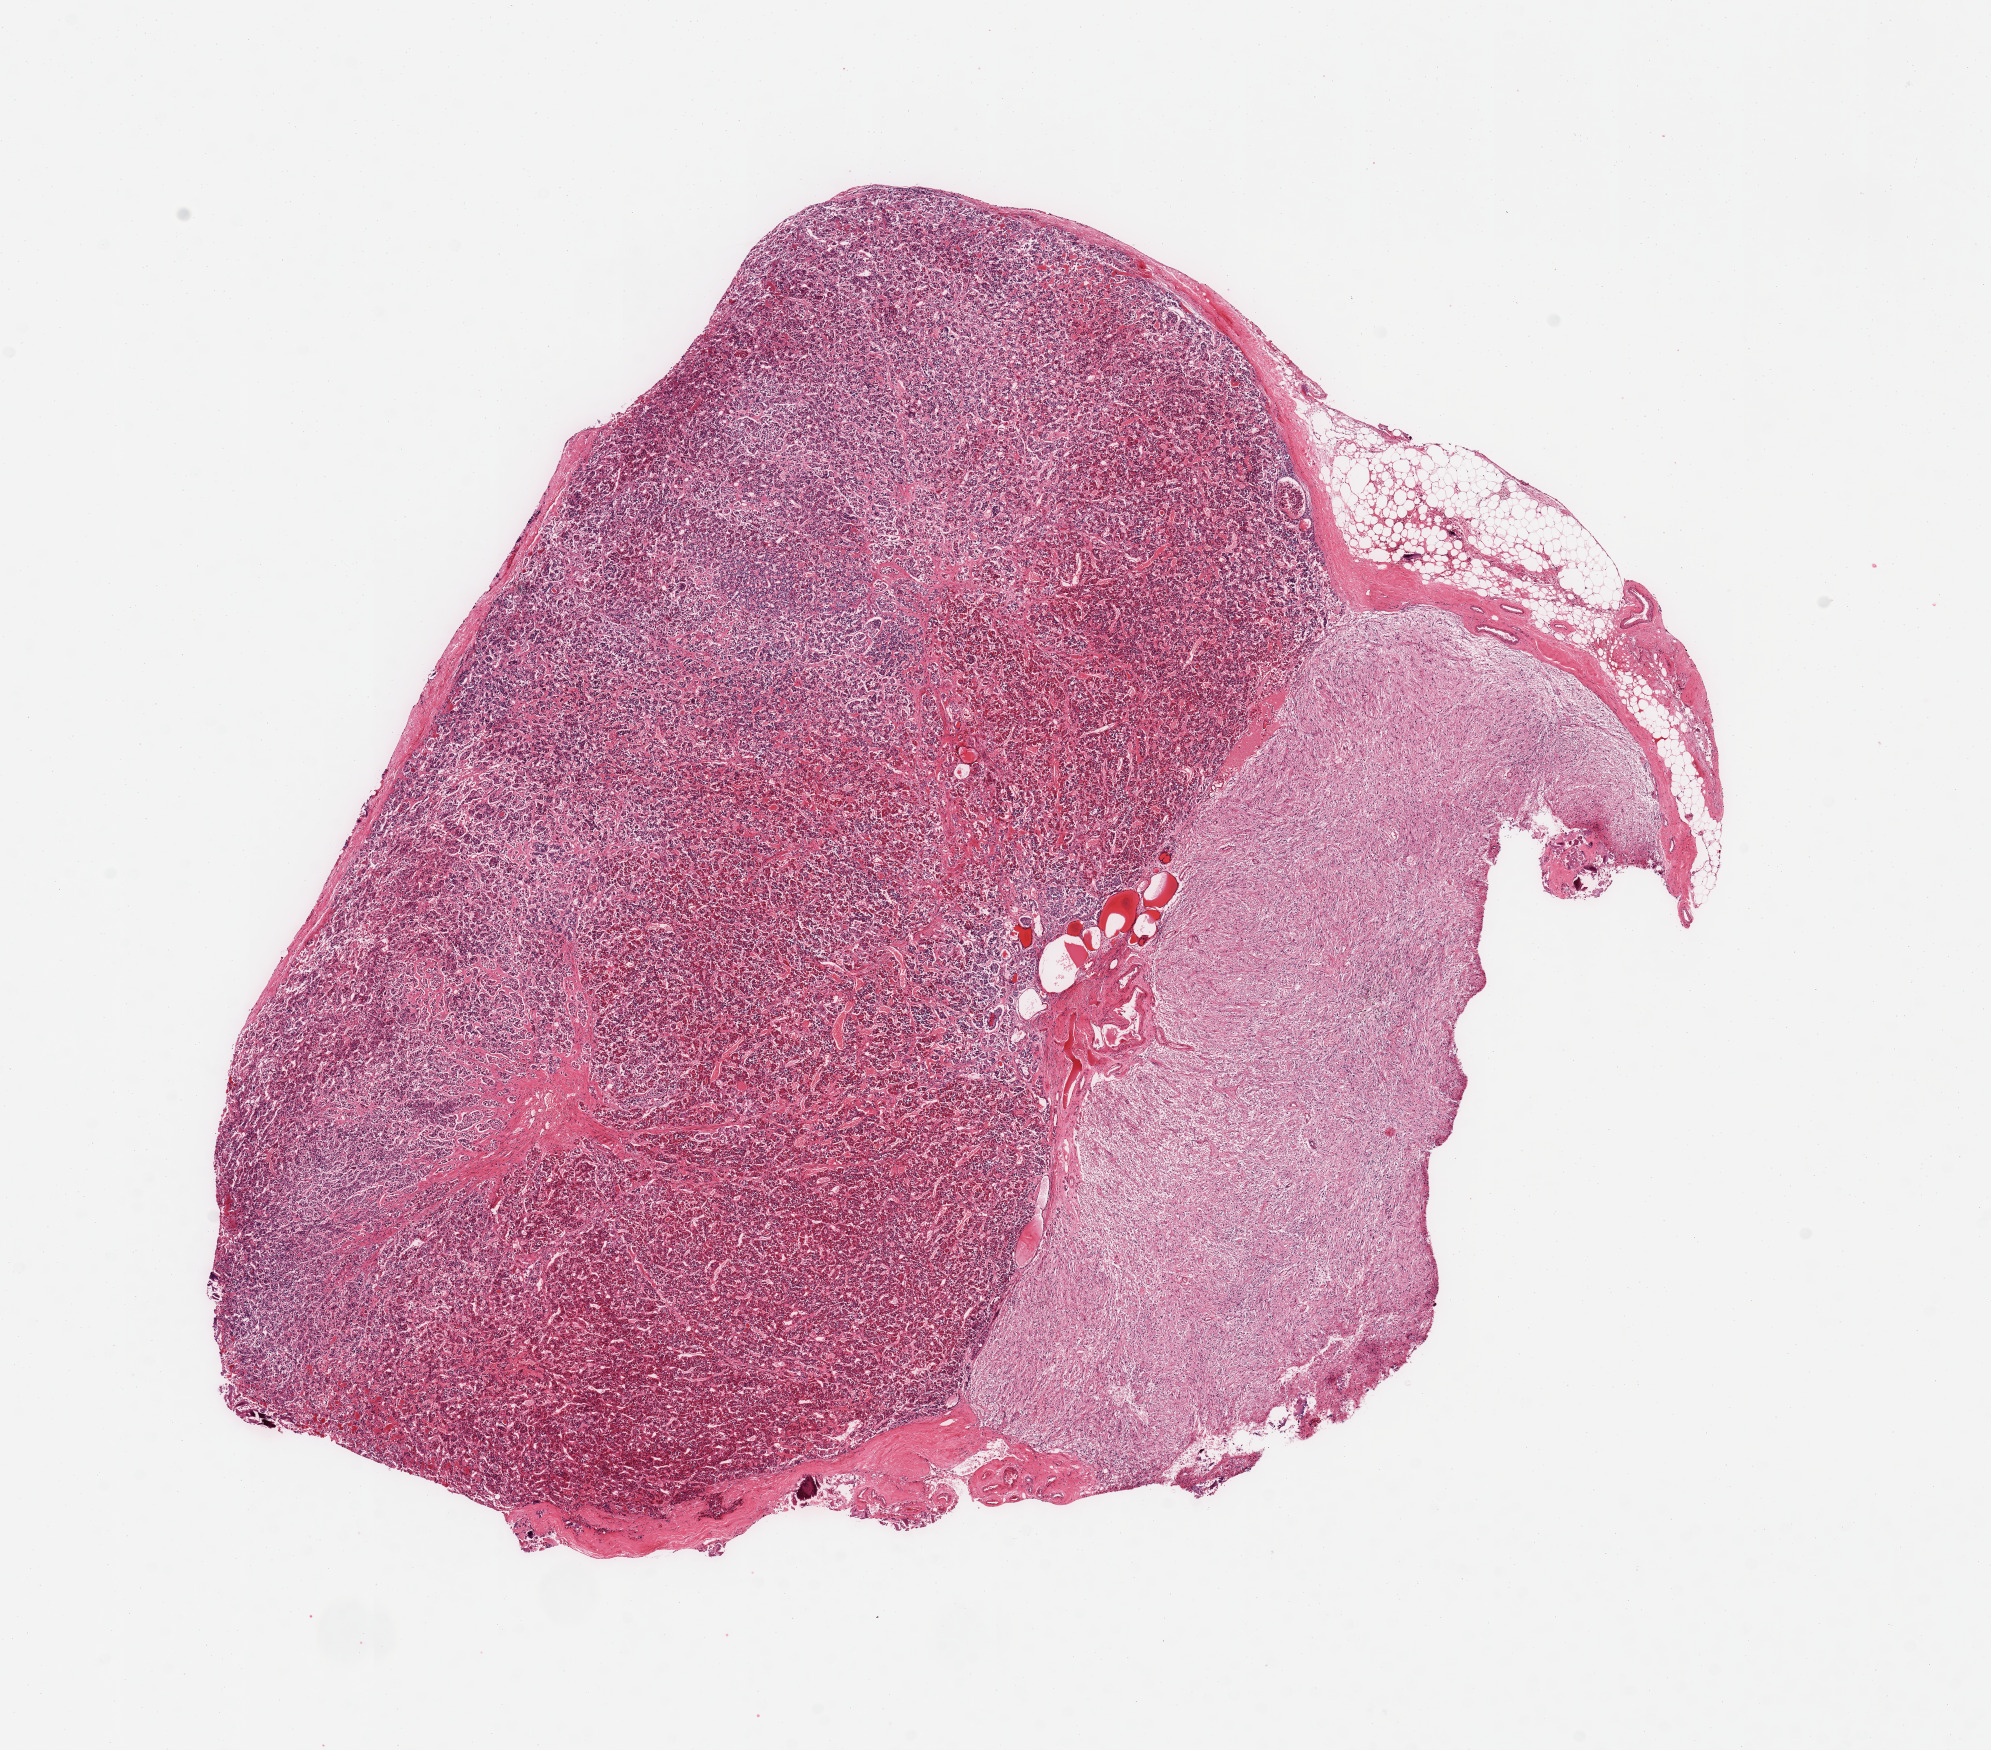
Hematoxylin and eosin (H&E) whole-slide image, a low-resolution overview of the entire scanned area, about 15.8 x 13.8 mm; PAXgene-fixed, paraffin-embedded tissue; target tissue: pituitary; donor tissue sample.
Review note (as recorded): 1 piece; adenohypophysis and neurohypophysis, small portion of attached fat (~5%).